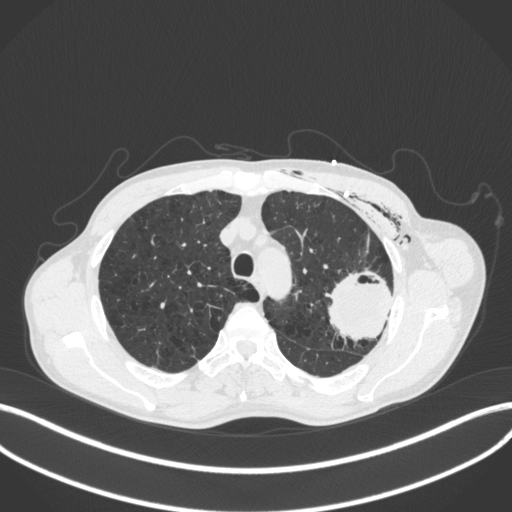
Chest CT, one axial slice. Slice 310 of 416 in the series (ordered by position). Reconstruction kernel B31f. Lung window (W 1500 / L -600 HU). 1 mm slice thickness. 512 × 512 image matrix. Patient: male, 58 years. Case-level facts recorded for this patient, not image findings: clinical TNM (as recorded): T3 N0 M0.
Structures marked on this image (rectangle marked by the reading radiologist):
- lung tumour (recorded histology: adenocarcinoma): bounding box (x1, y1, x2, y2) in pixels: (318, 268, 402, 340)